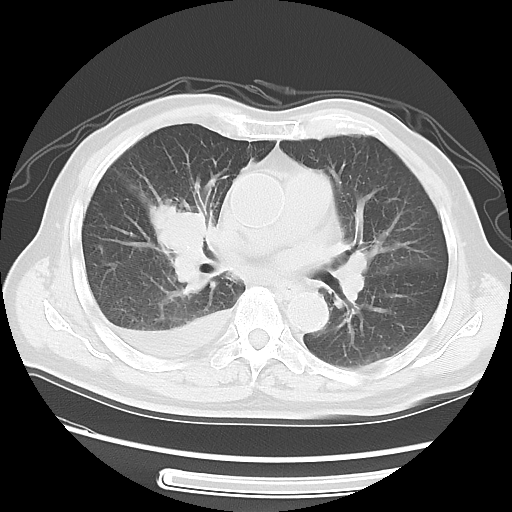
Chest CT, one axial slice. Slice 29 of 56 in the series (ordered by position). 120 kVp. Lung window (W 1500 / L -600 HU). 5 mm slice thickness. 512 × 512 image matrix, field of view 360 × 360 mm. Male patient, age 77 years. From the clinical record (not read from this slice): clinical TNM (as recorded): T3 N3 M1b; histopathological grade: G3.
Outlined on this slice (bounding box drawn by a radiologist):
- lung tumour (recorded histology: small cell carcinoma): bounding box [x1, y1, x2, y2] px = [142, 199, 221, 288]